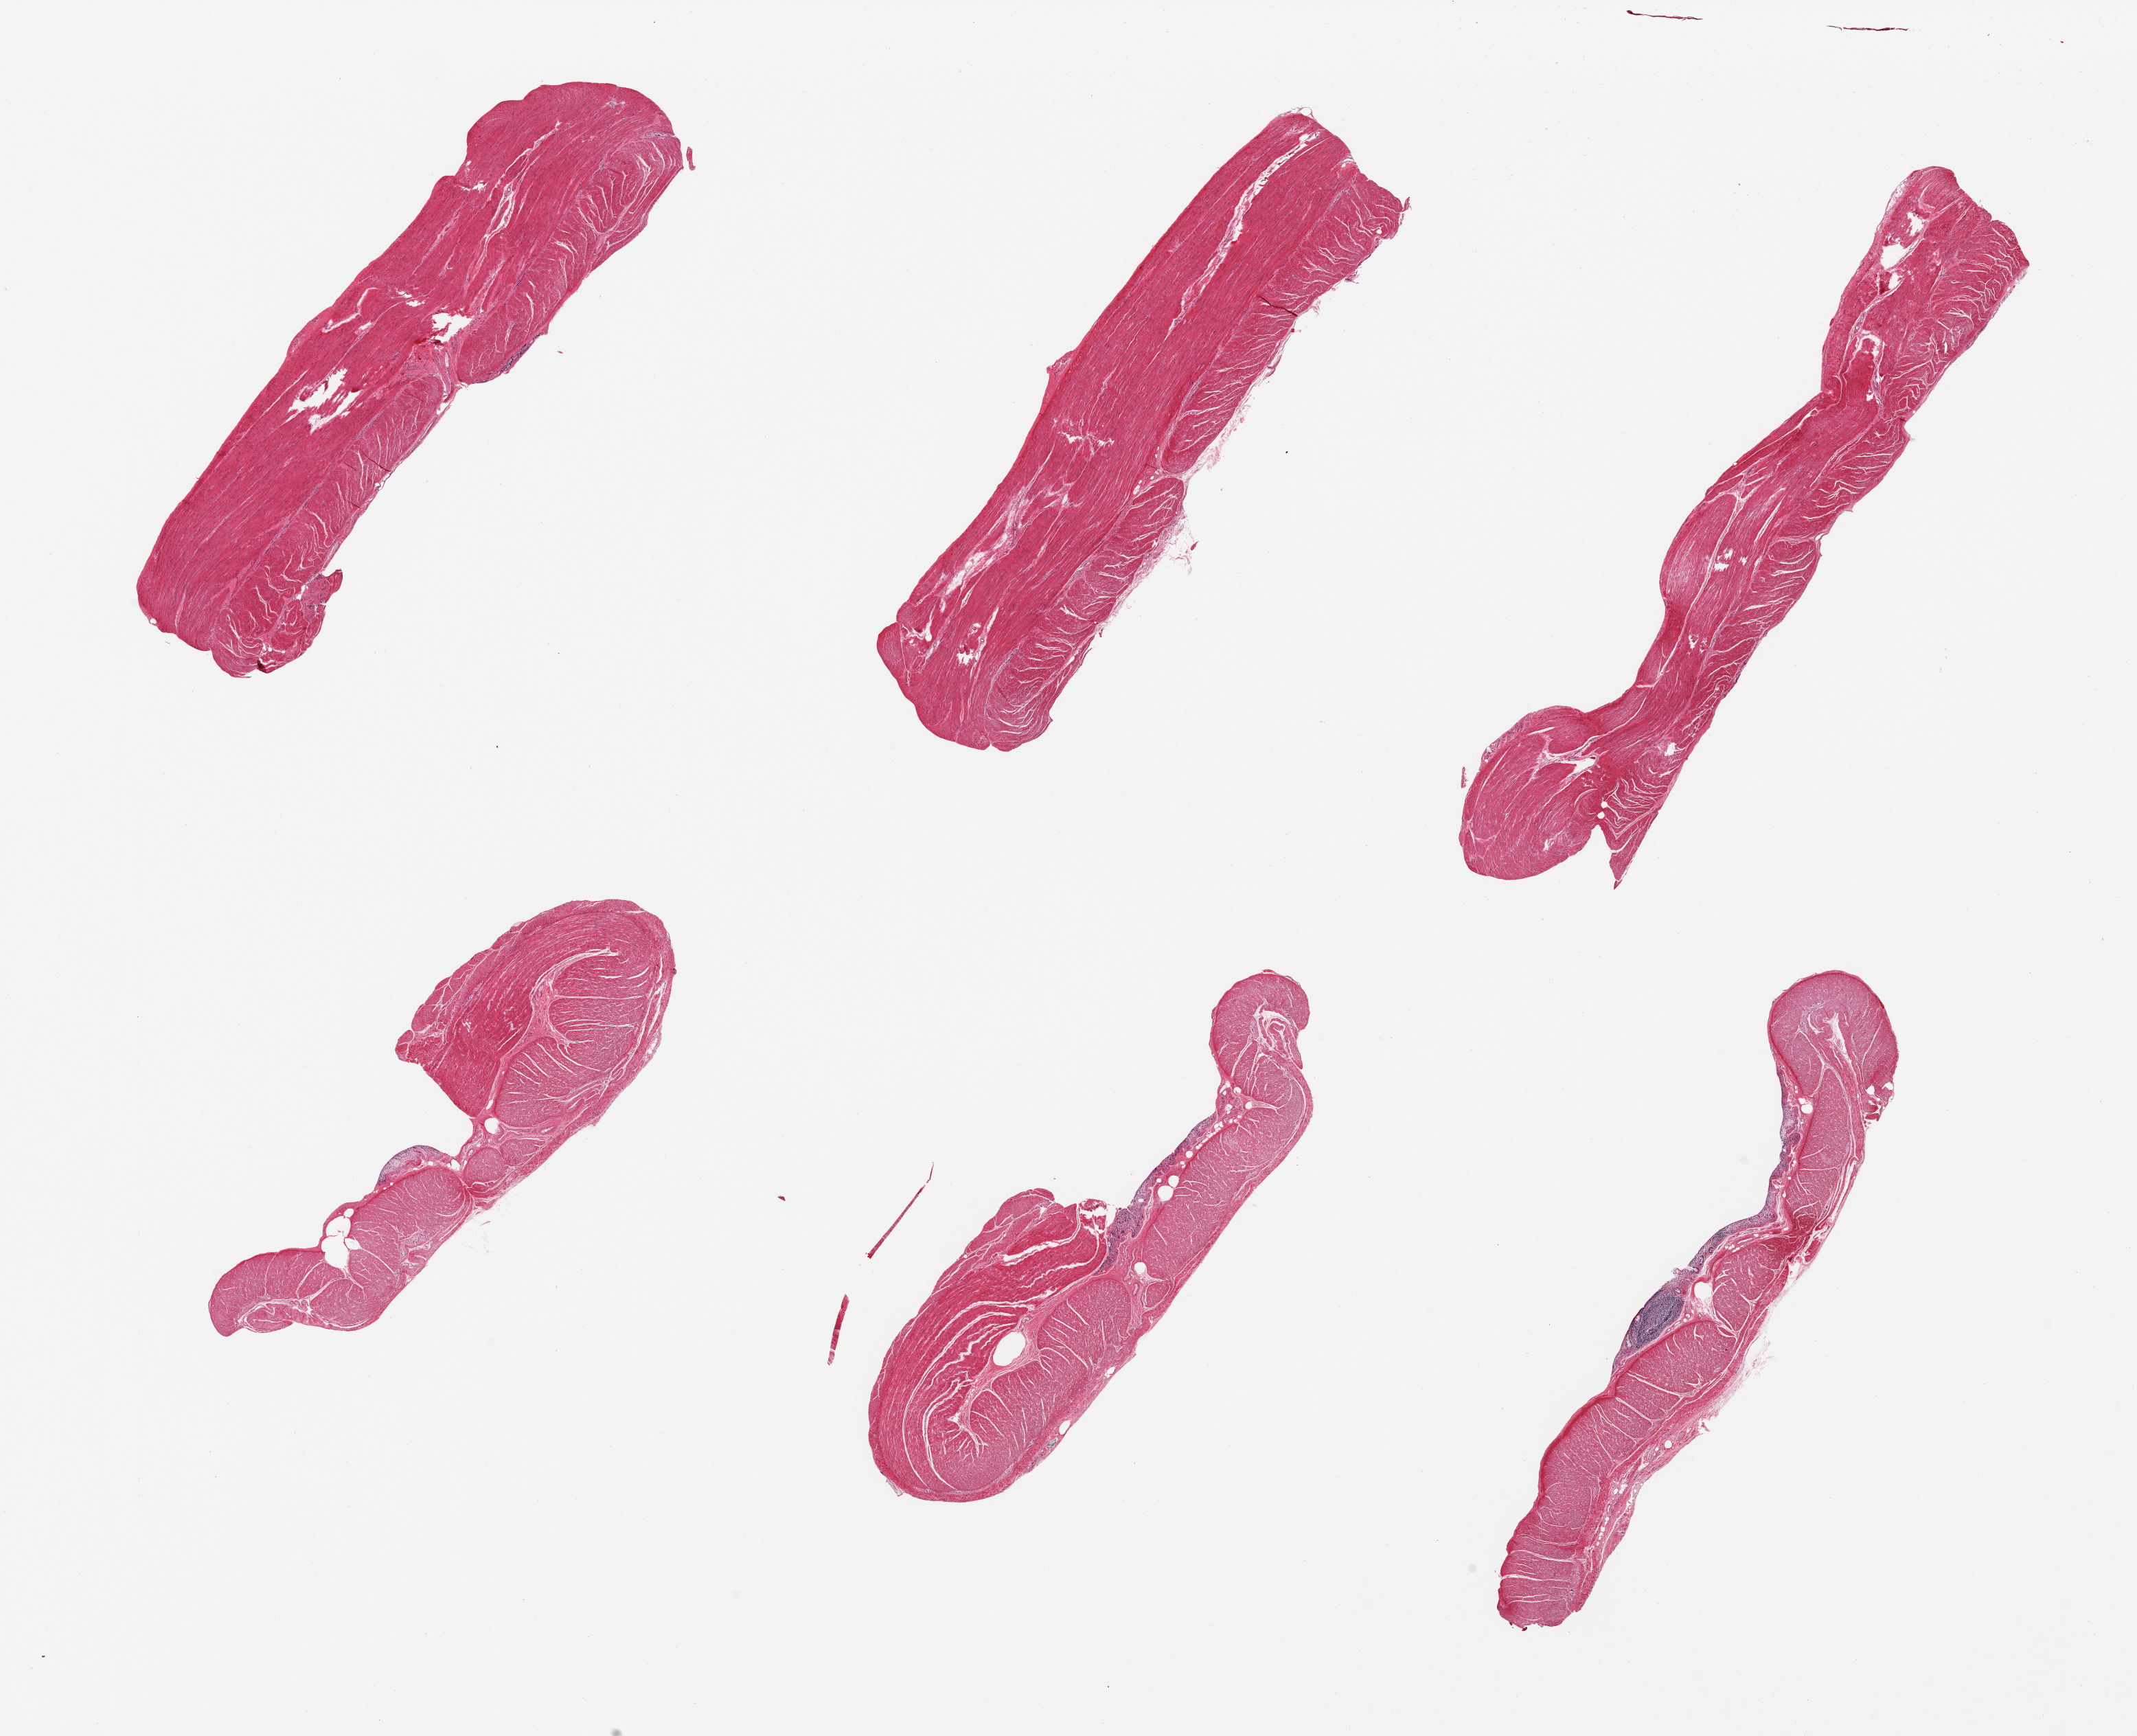
Haematoxylin and eosin whole-slide image, shown as a low-resolution overview of the whole scanned area (about 24.6 x 20.0 mm), PAXgene-fixed paraffin-embedded (PFPE) section, target tissue: sigmoid colon, donor tissue sample. Donor sex: male.
Pathologist's review note for this sample: 6 pieces; well trimmed muscularis; small focus of mucosa.